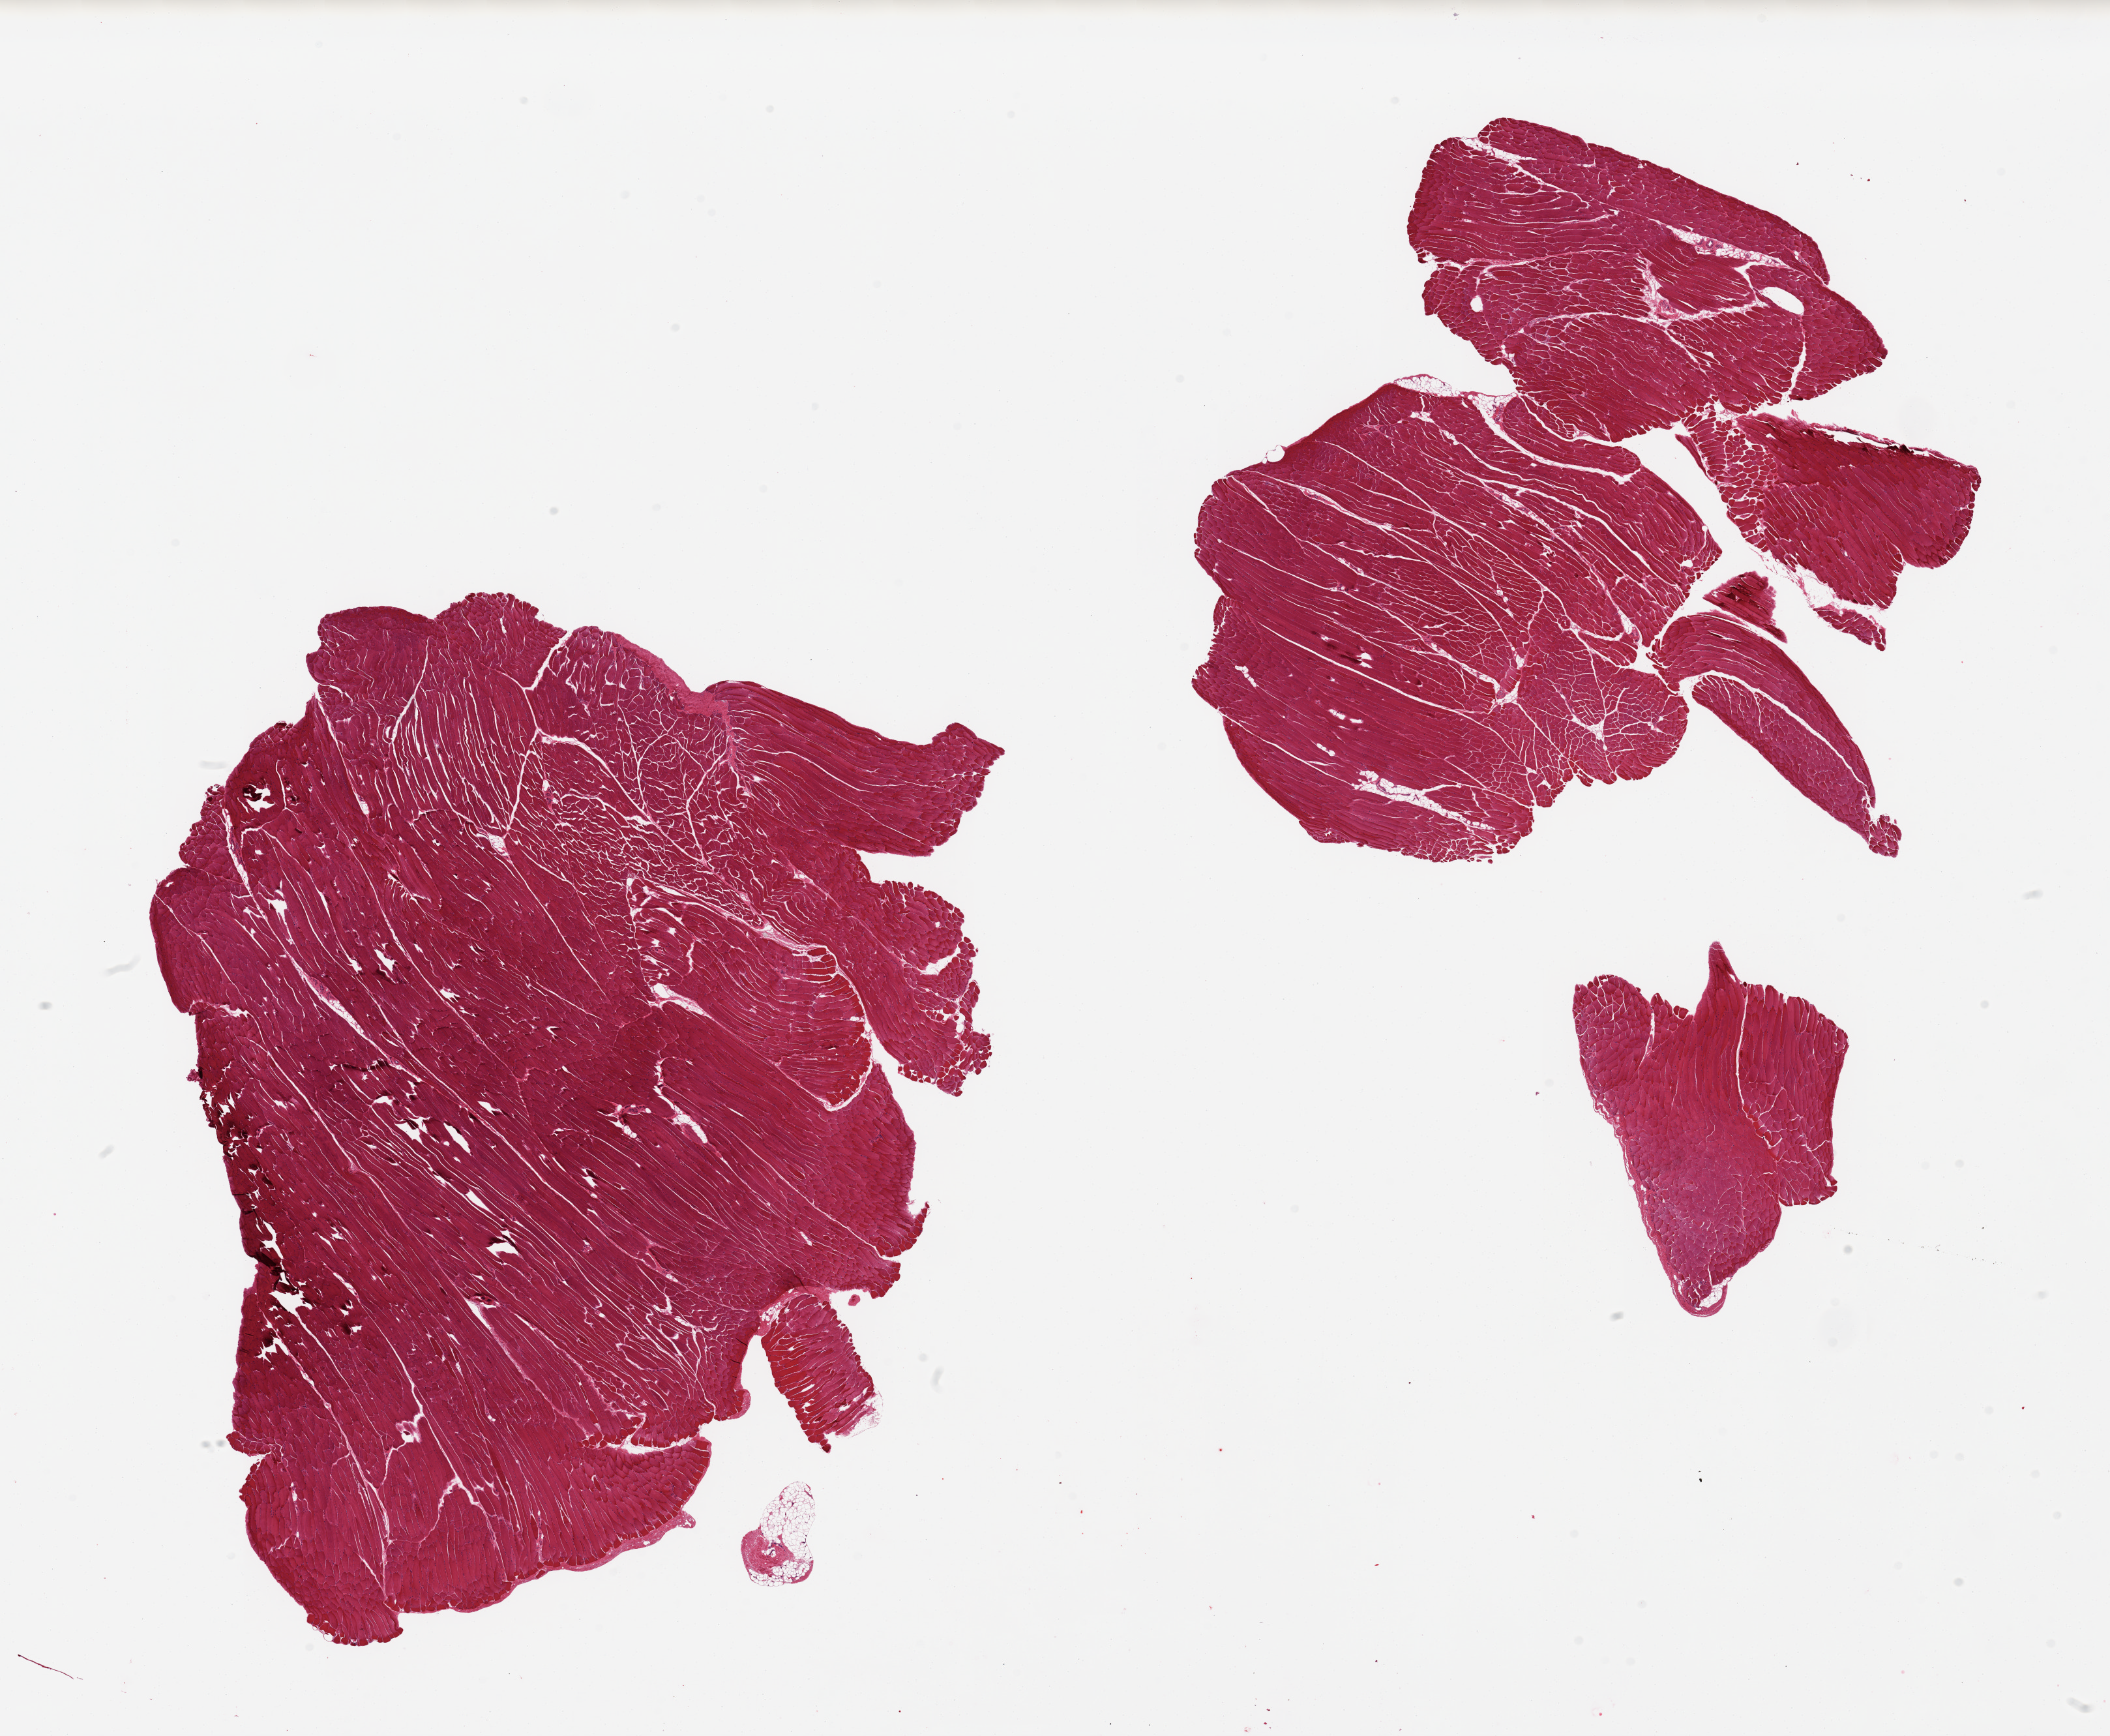
Whole-slide image, hematoxylin and eosin (H&E) stain, shown as a low-resolution overview of the whole scanned area (about 25.6 x 21.1 mm, acquisition: 20x scan), PAXgene-fixed, paraffin-embedded tissue, sampled site (target tissue): skeletal muscle, donor tissue sample.
* review note (as recorded): 2 pieces